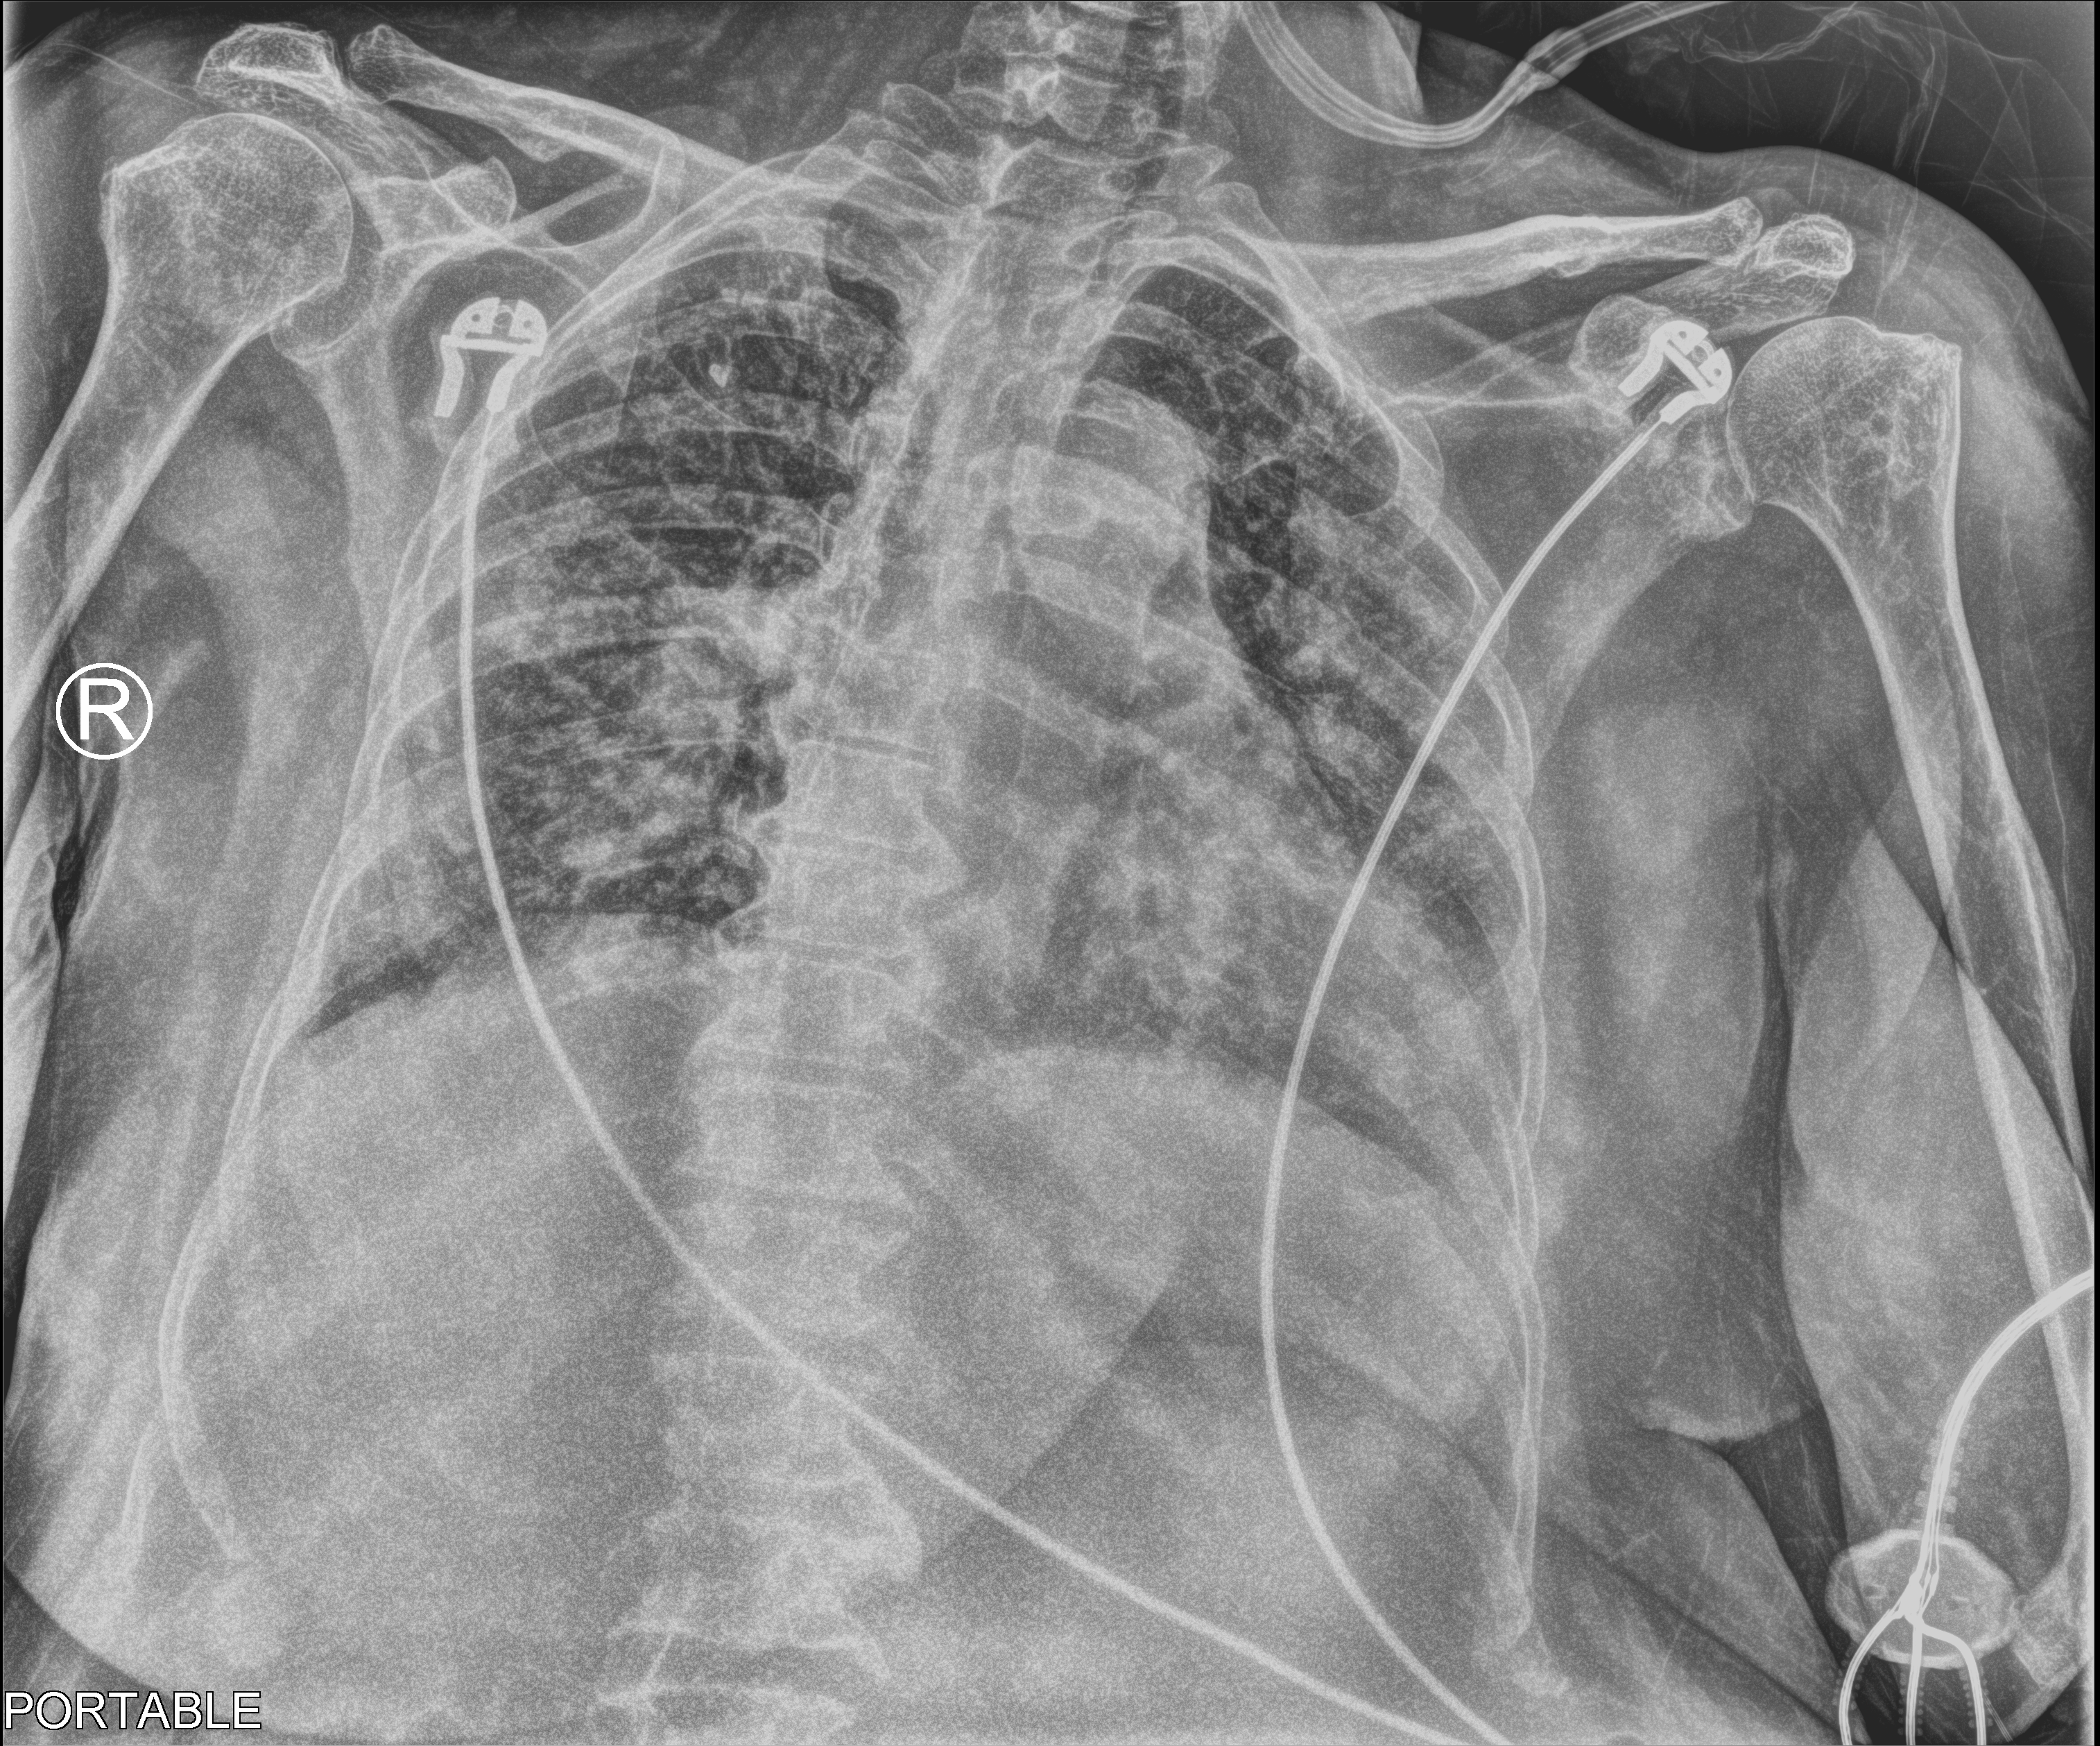
Bedside chest radiograph (computed radiography); anteroposterior (AP) projection. Female patient hospitalised with COVID-19, age 75–90 years.
From the hospital-stay record, not from the radiograph (when in the stay this image was taken is not recorded):
- admitted to intensive care during this hospital stay: yes
- length of hospital stay: 37 days
- mechanically ventilated during this hospital stay: no